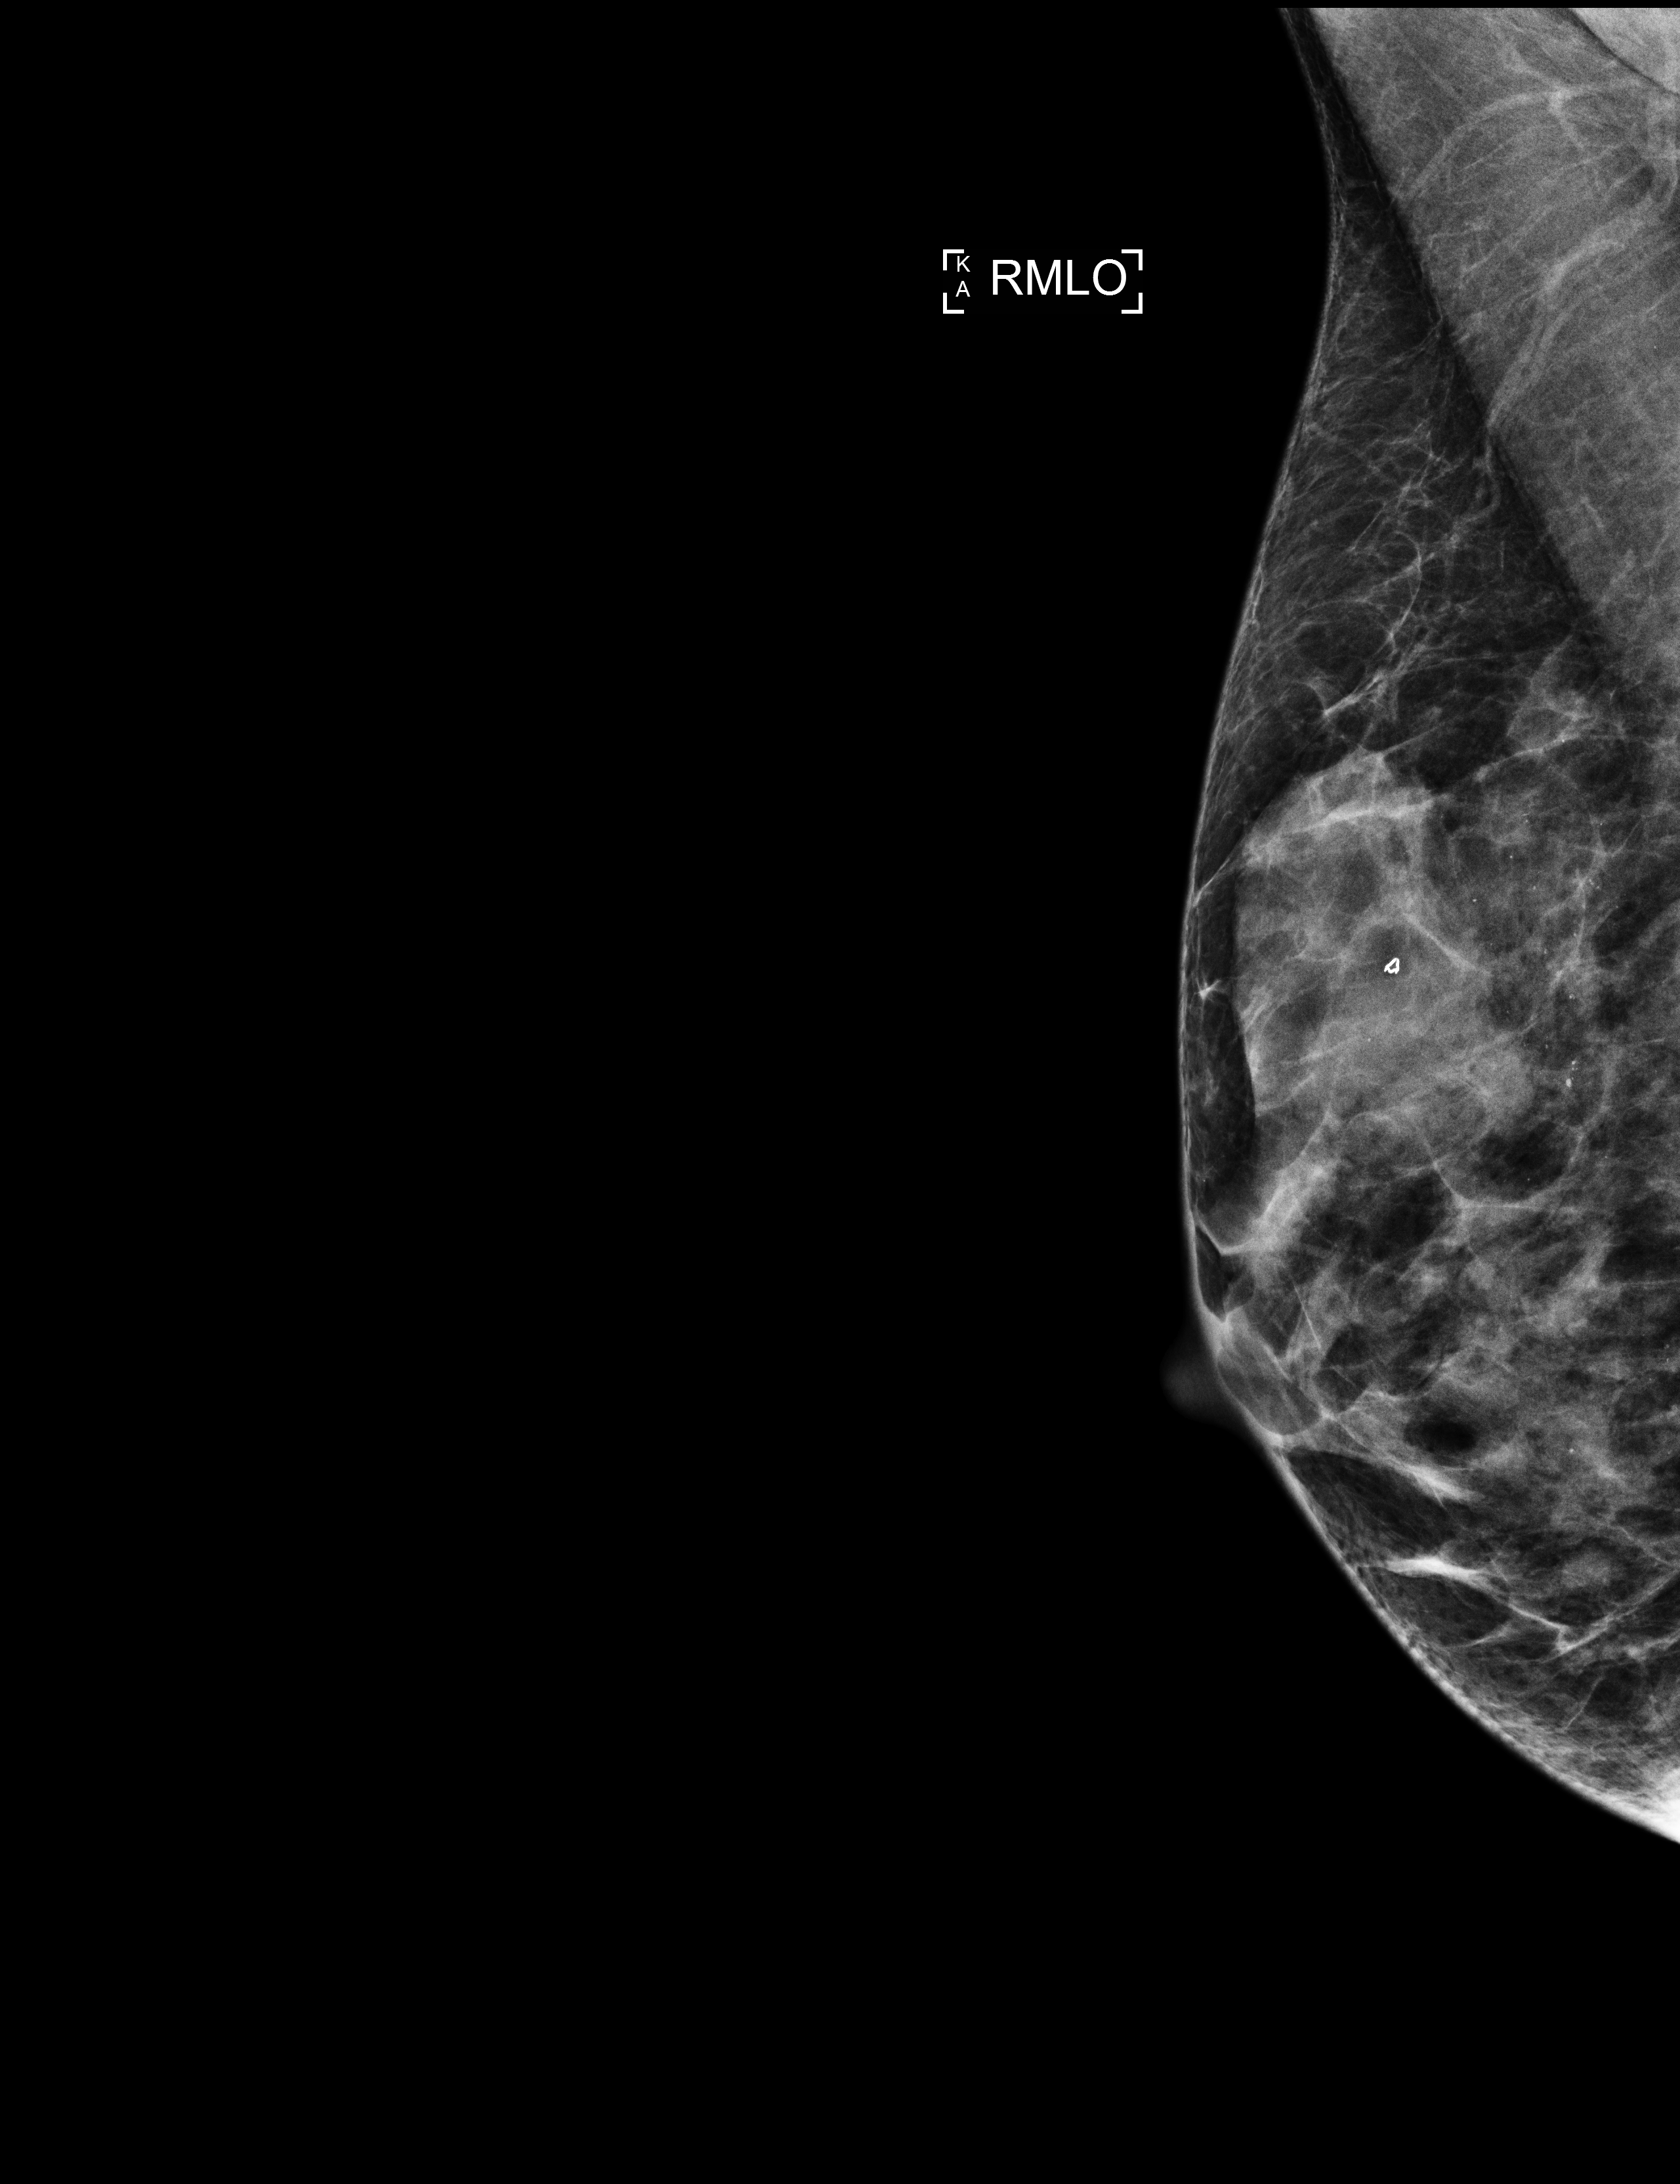
Annual screening mammography examination; system: Selenia Dimensions. Patient aged 59 years (female).
Image type: full-field digital mammogram. Breast: right. Projection: mediolateral oblique (MLO) view.